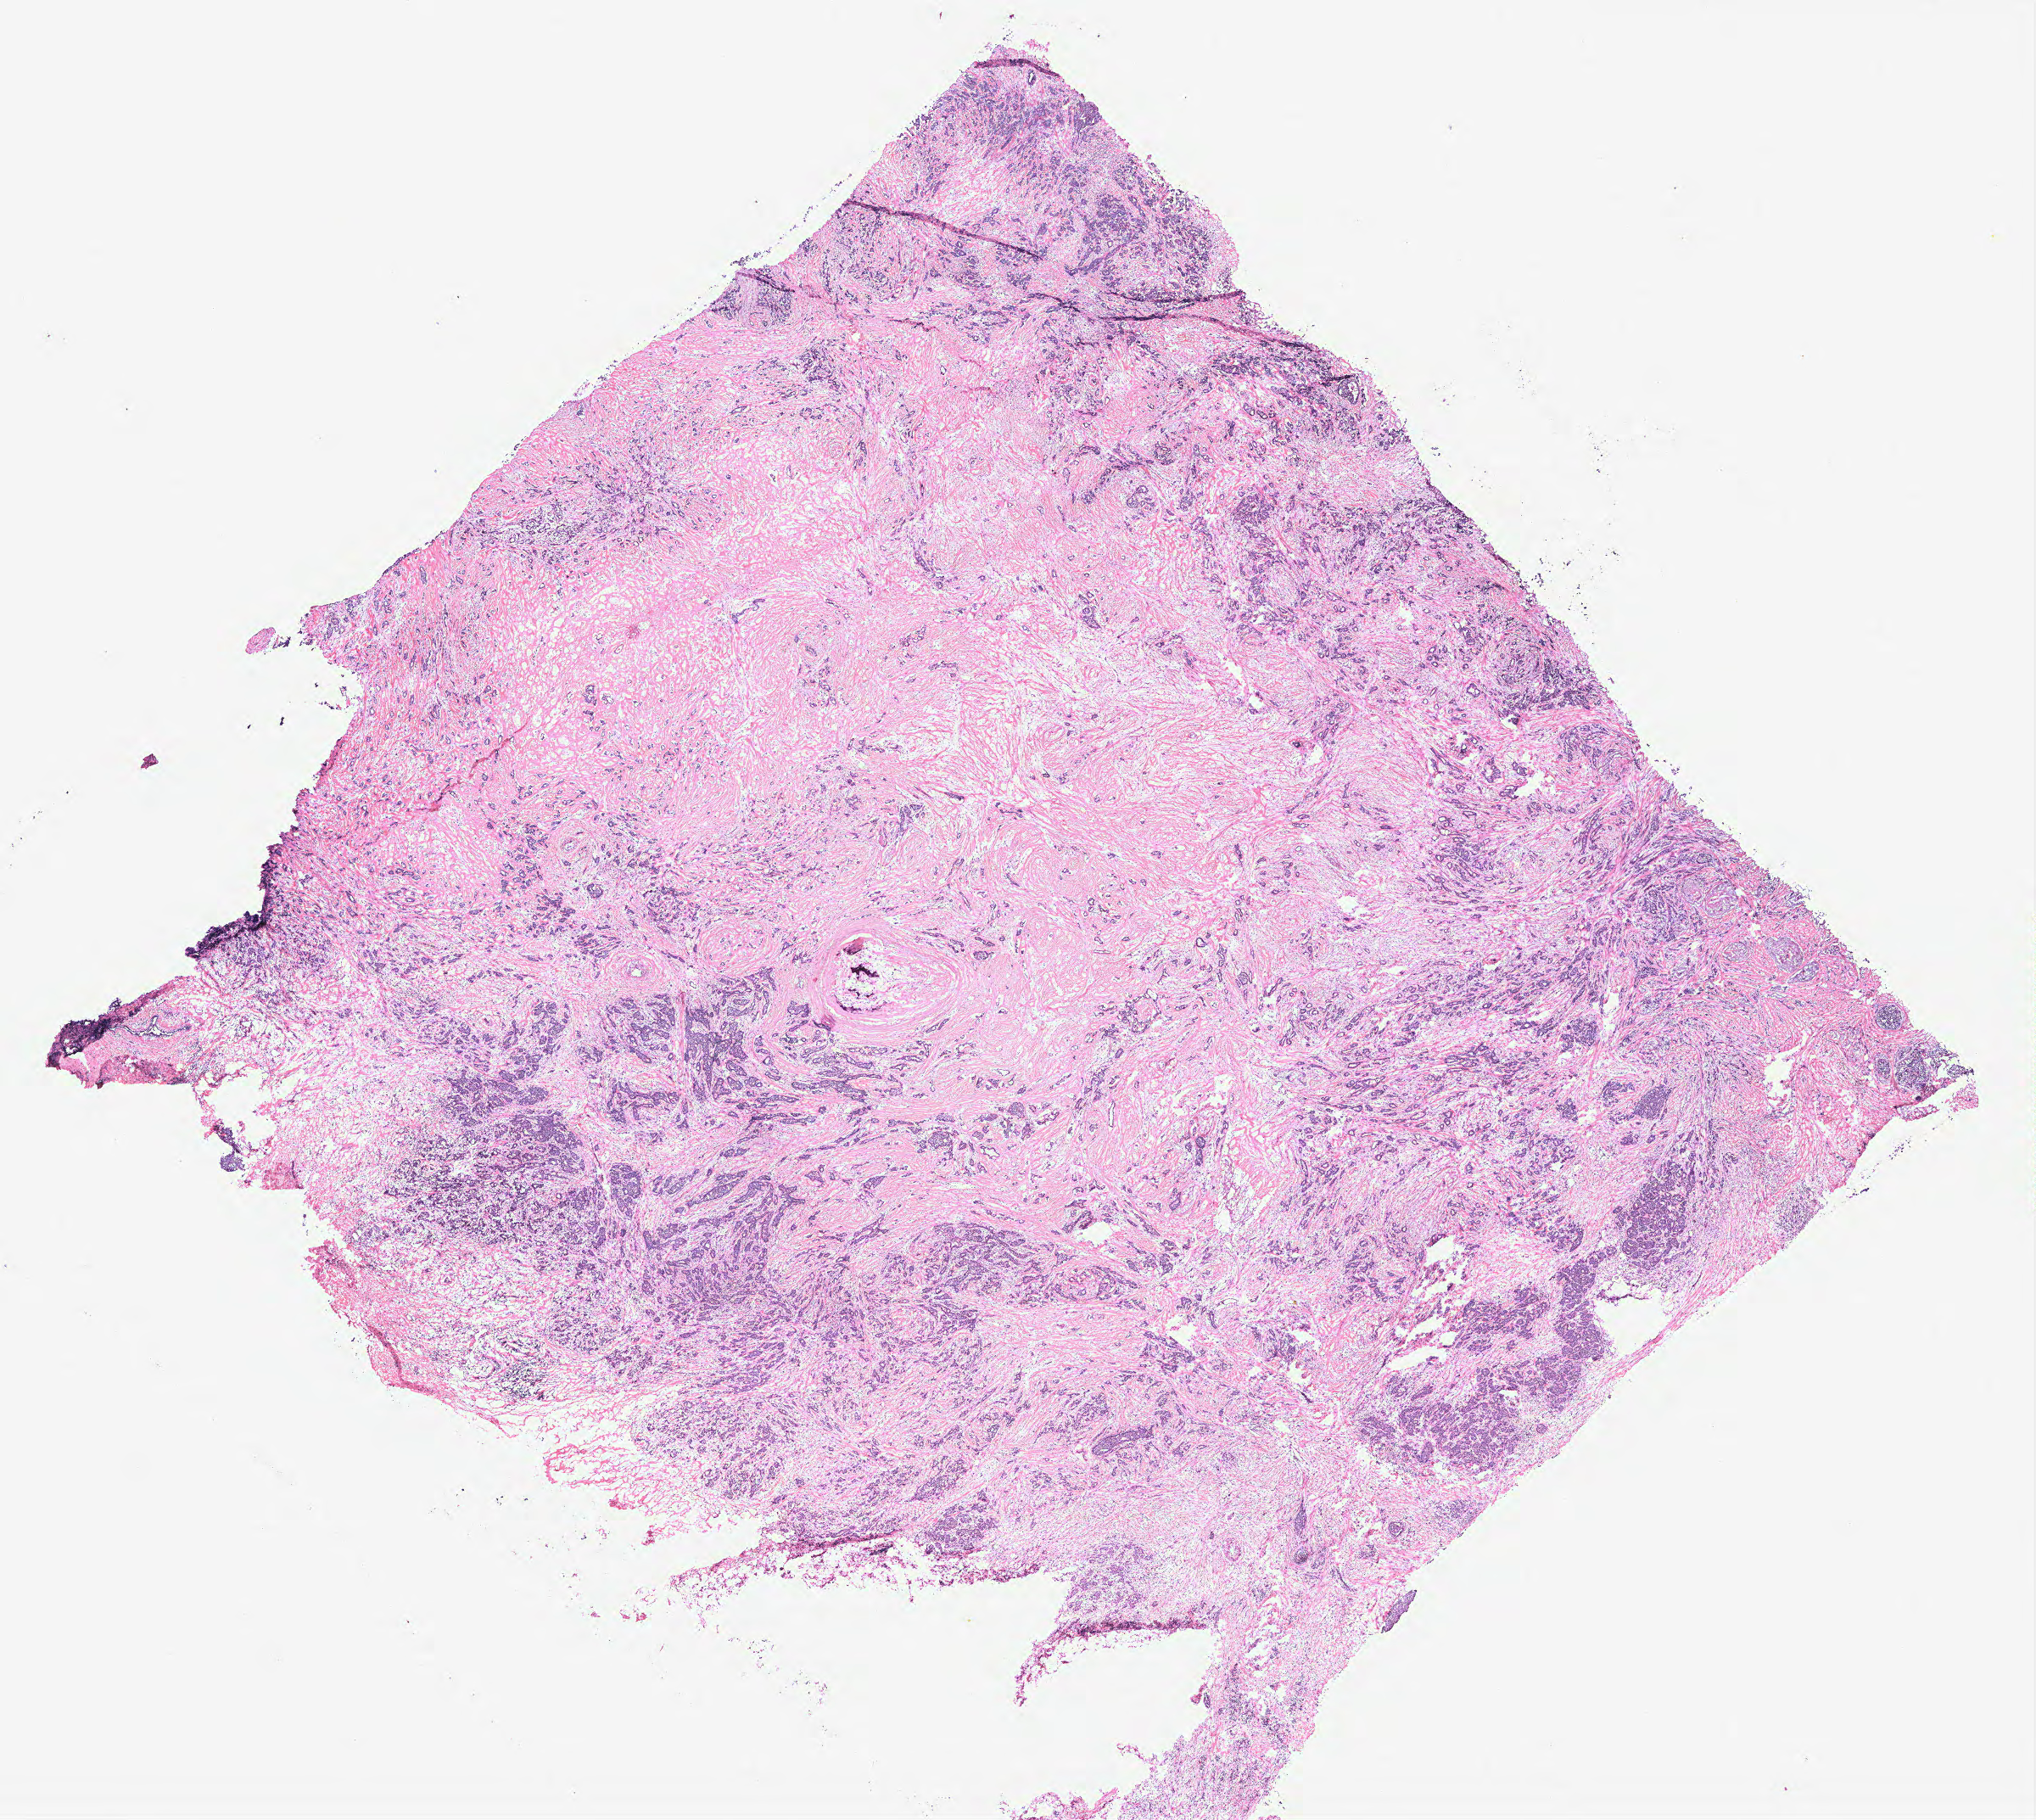
Whole-slide histology image, Hematoxylin and eosin (H&E) stained, a low-resolution overview of the entire scanned area, about 19.2 x 17.2 mm (from a 40x scan); breast, tissue type not recorded. Female, 66 y/o.
- patient diagnosis: Infiltrating duct carcinoma, NOS